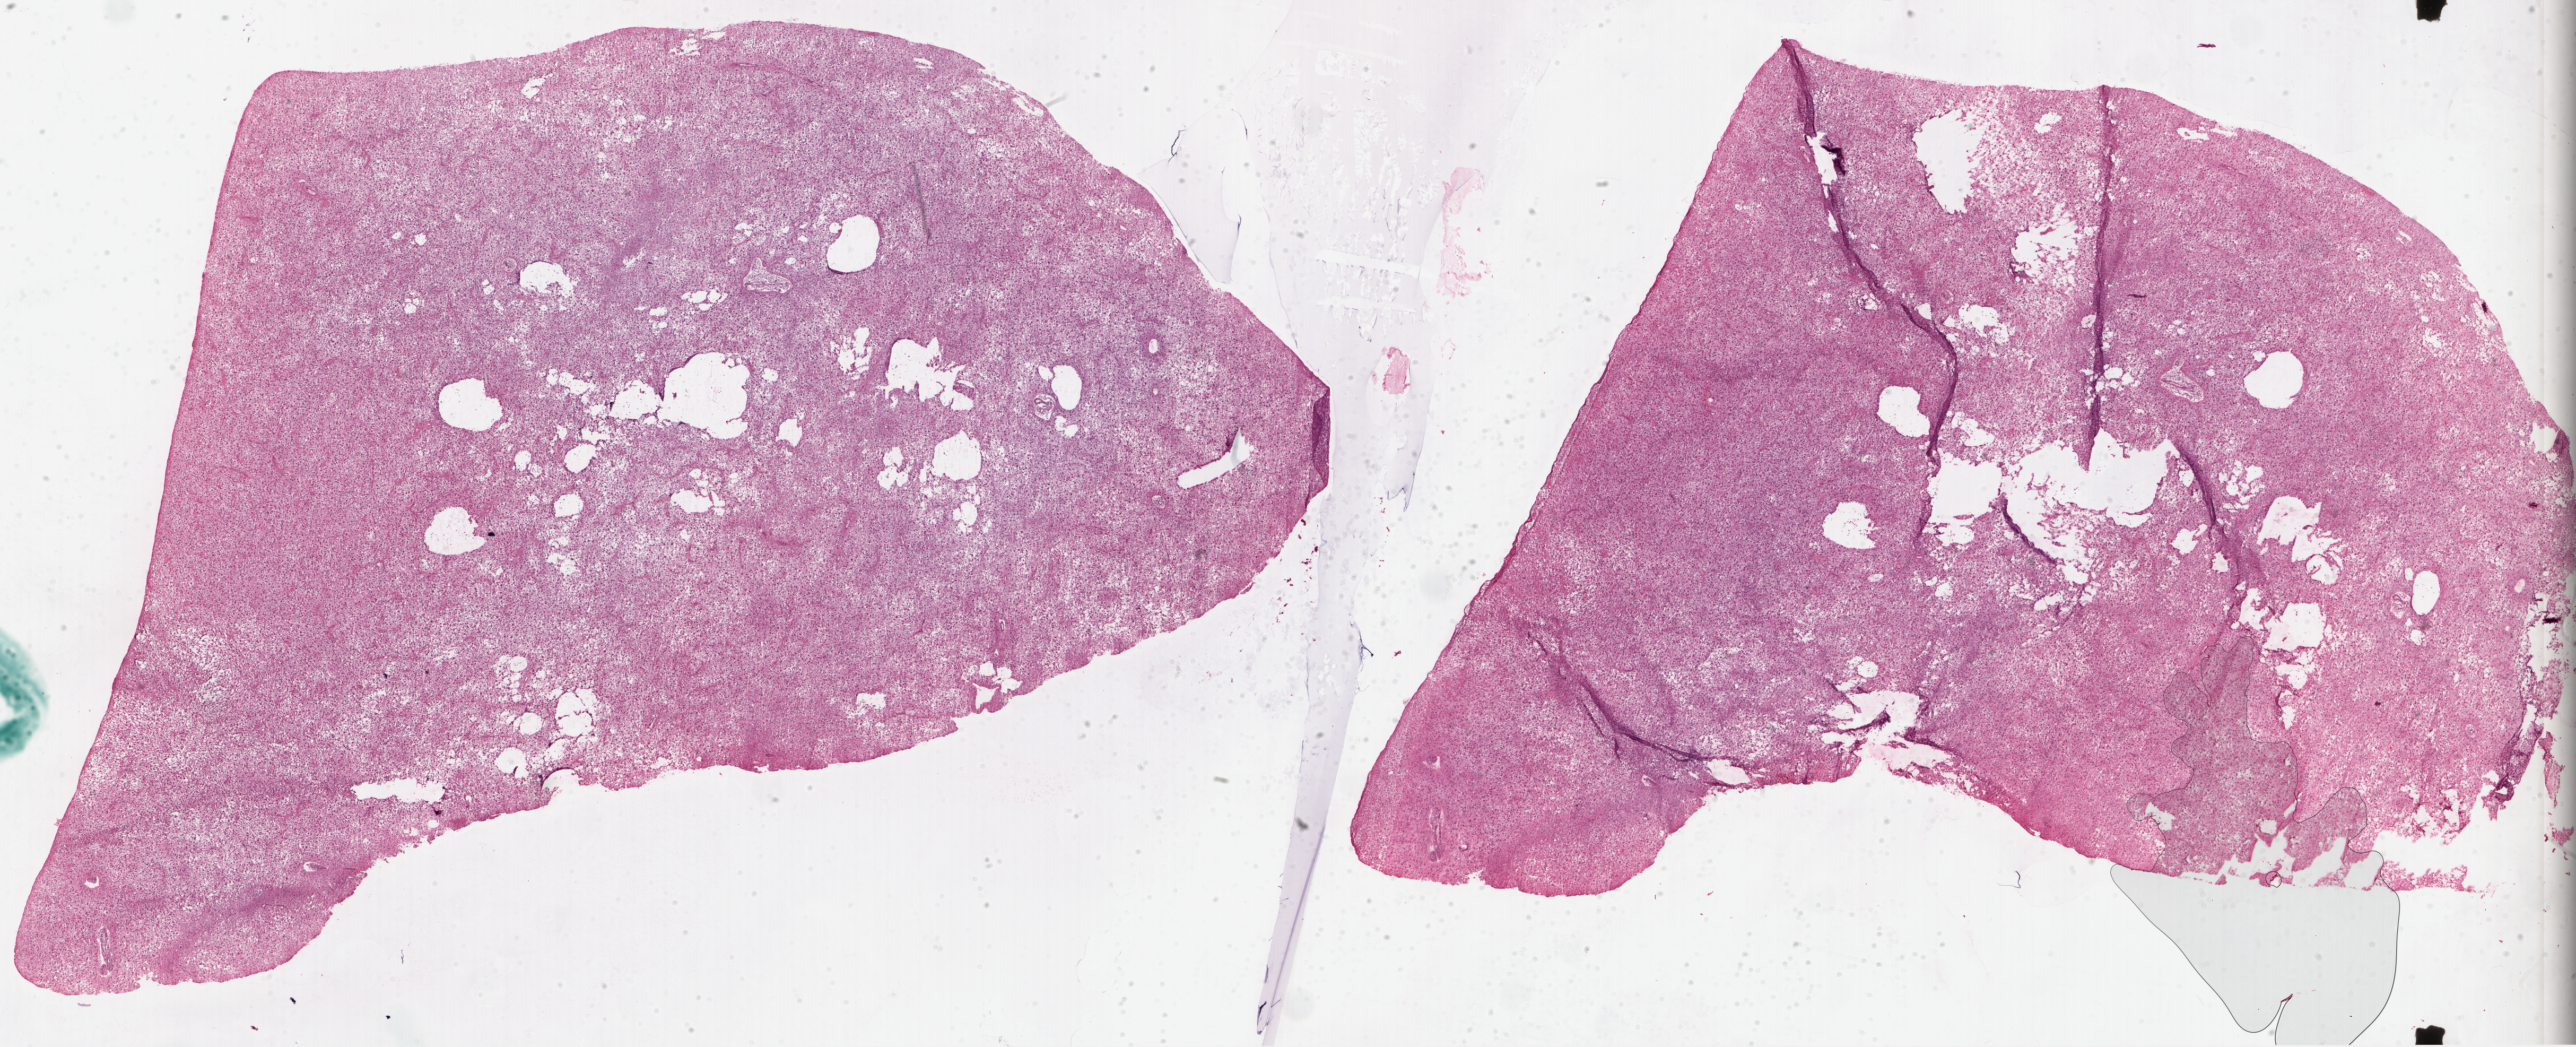
Digitized Hematoxylin and eosin (H&E) stained tissue section (whole slide), shown as a low-resolution overview of the whole scanned area (about 39.2 x 15.9 mm, acquisition: 20x scan); frozen section from the top of the tissue portion; sample: primary tumour, brain. Female, age 27 years at initial diagnosis. Pathologist review of this section (percent, as recorded): tumour cells 100%, tumour nuclei 100%, normal cells 0%, stromal cells 0%, necrosis 0%.
Diagnosis: Glioblastoma.